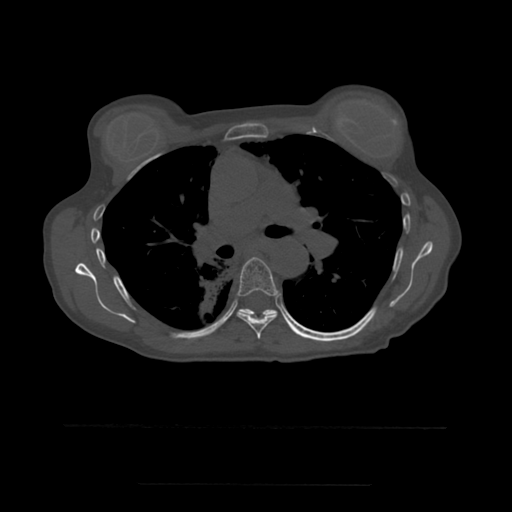
CT including the spine, one axial slice; position 372 of 544 along the scan axis; bone window (W 1800 / L 400 HU); 1.25 mm slice thickness; 512 × 512 image matrix, field of view 350 × 350 mm. Patient age 58 years. From the clinical record (not read from this slice): primary cancer: lung.
Annotated regions visible in this slice (semi-automatically segmented with operator editing):
- T6 vertebra: bounding box [x1, y1, x2, y2] px = [237, 258, 282, 339]
- T7 vertebra: [241, 309, 290, 326]